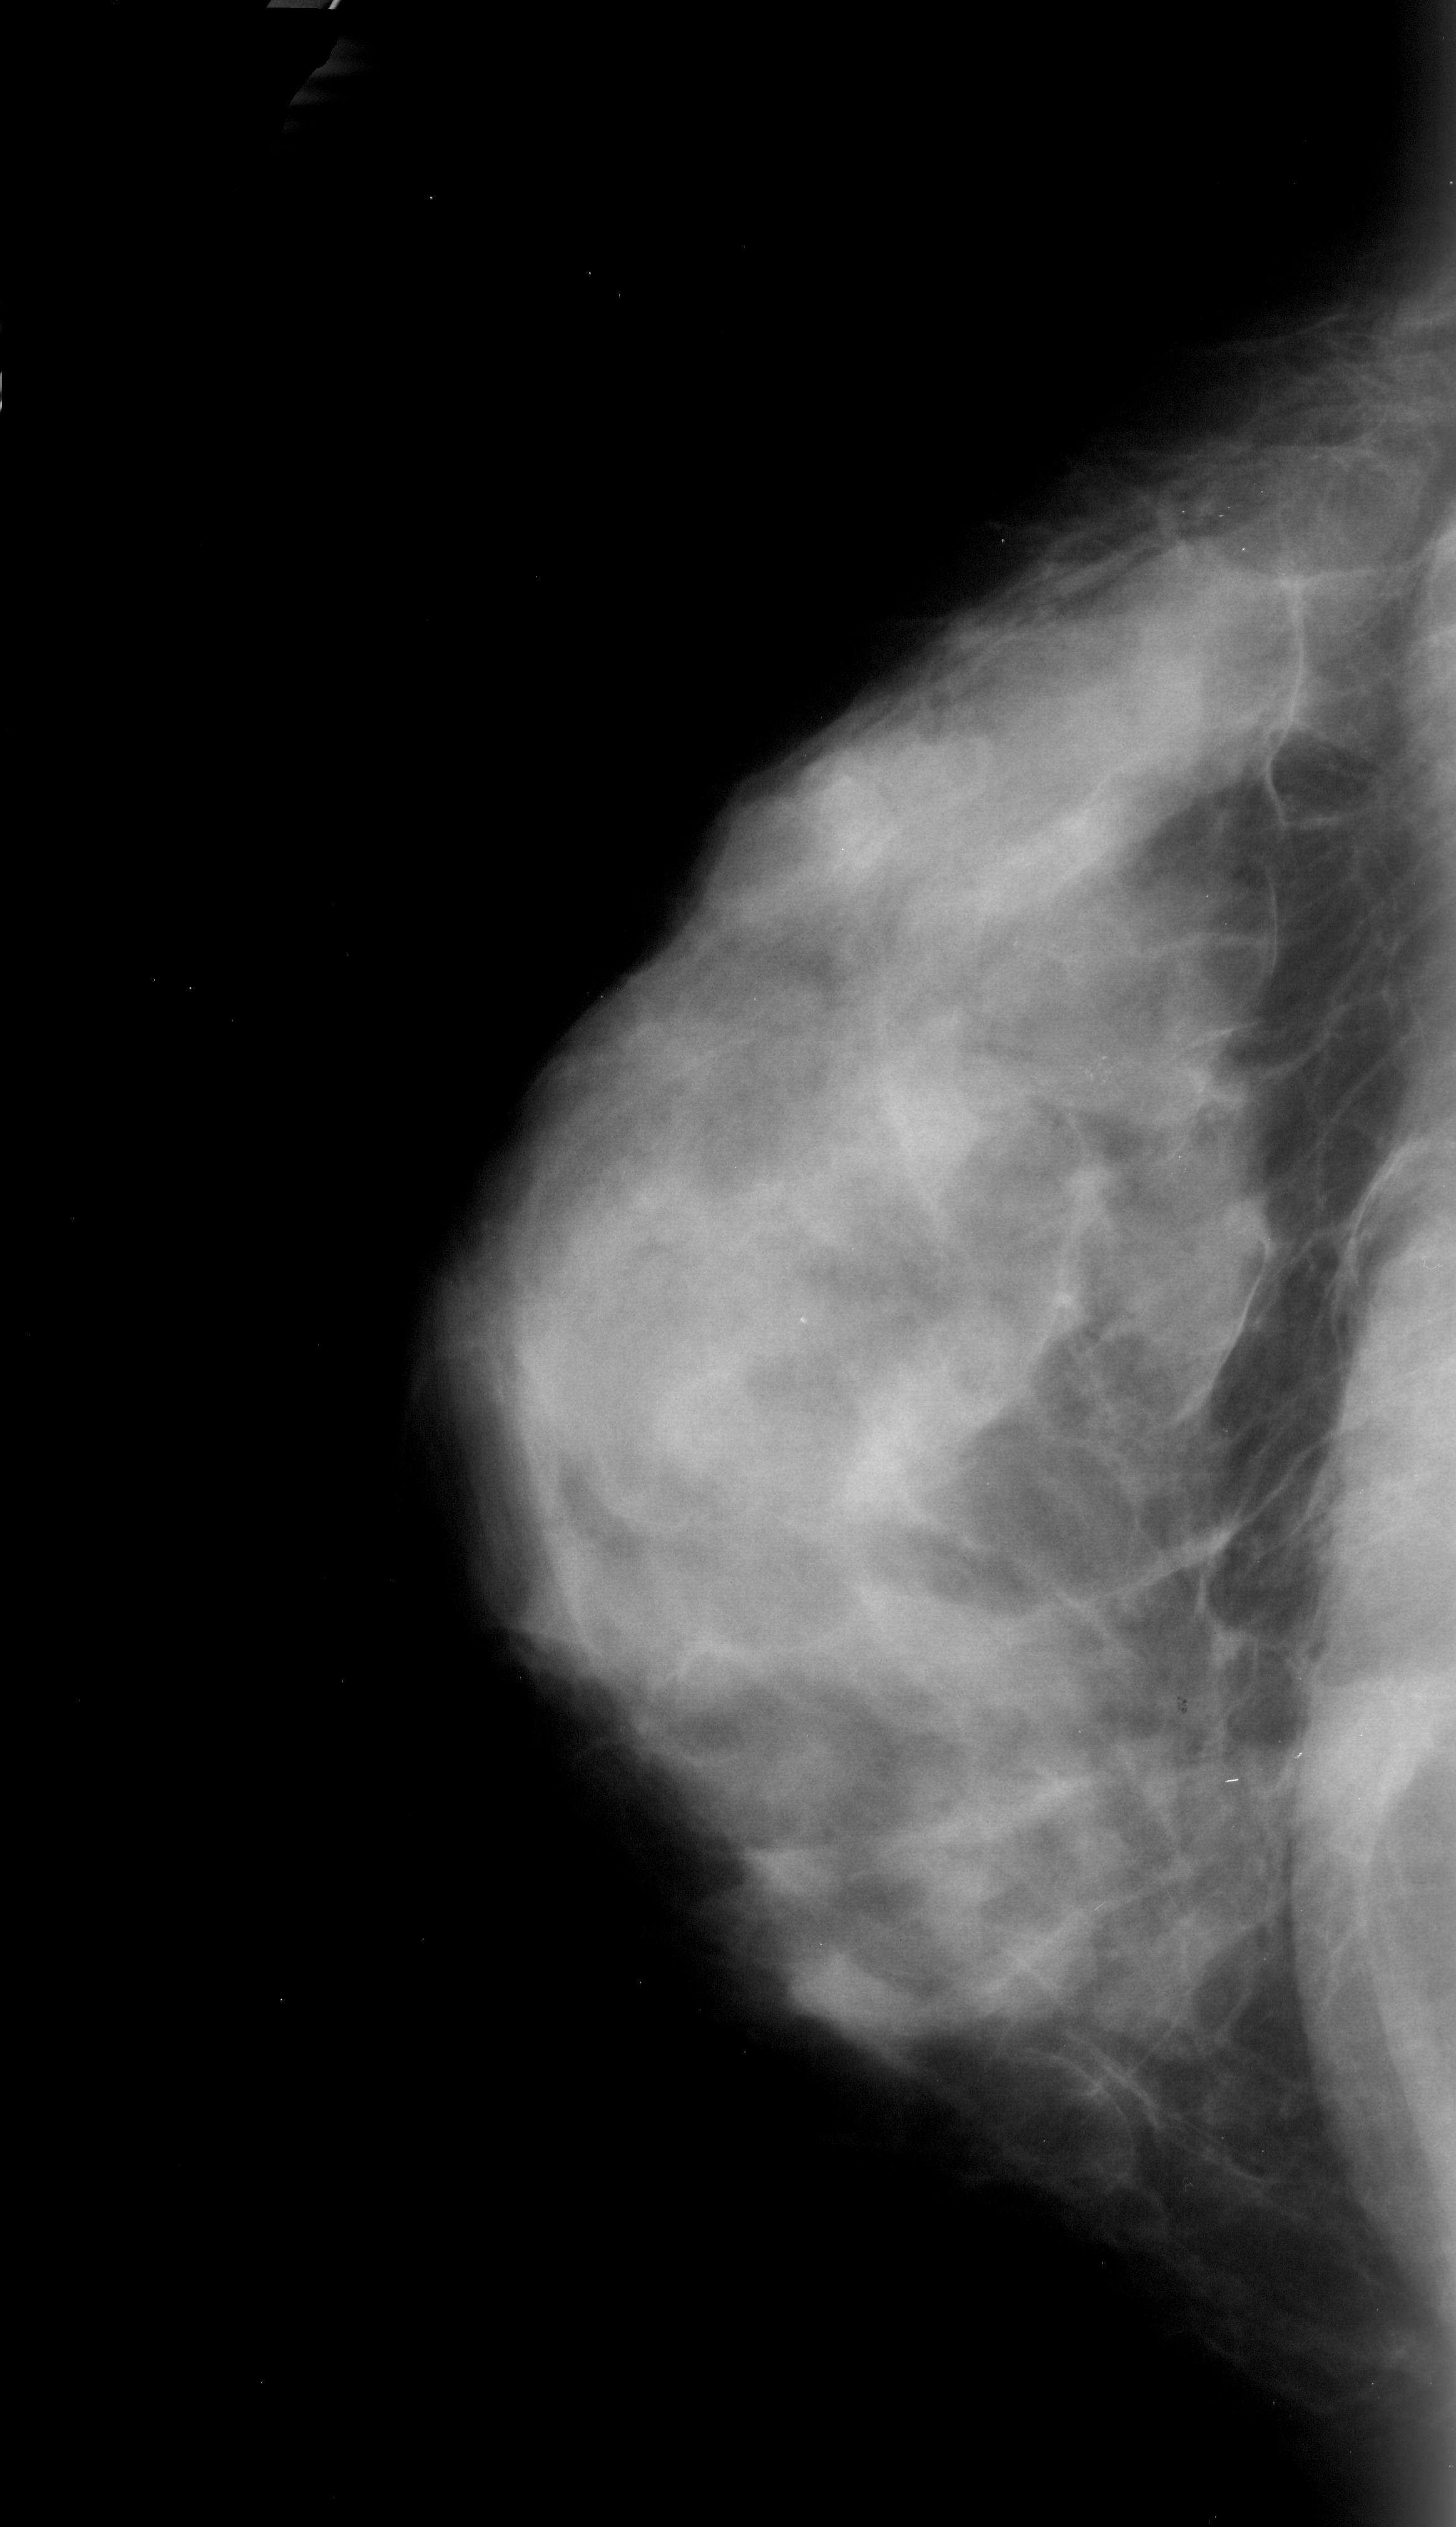
Mammogram (digitized film), left breast, CC view, BI-RADS breast density category 4 (scale 1–4).
Finding: calcifications, morphology punctate, distribution clustered; BI-RADS assessment category 4; subtlety rating 1 on a 1 (subtle) to 5 (obvious) scale; pathology result (as recorded, not read from the image): malignant.